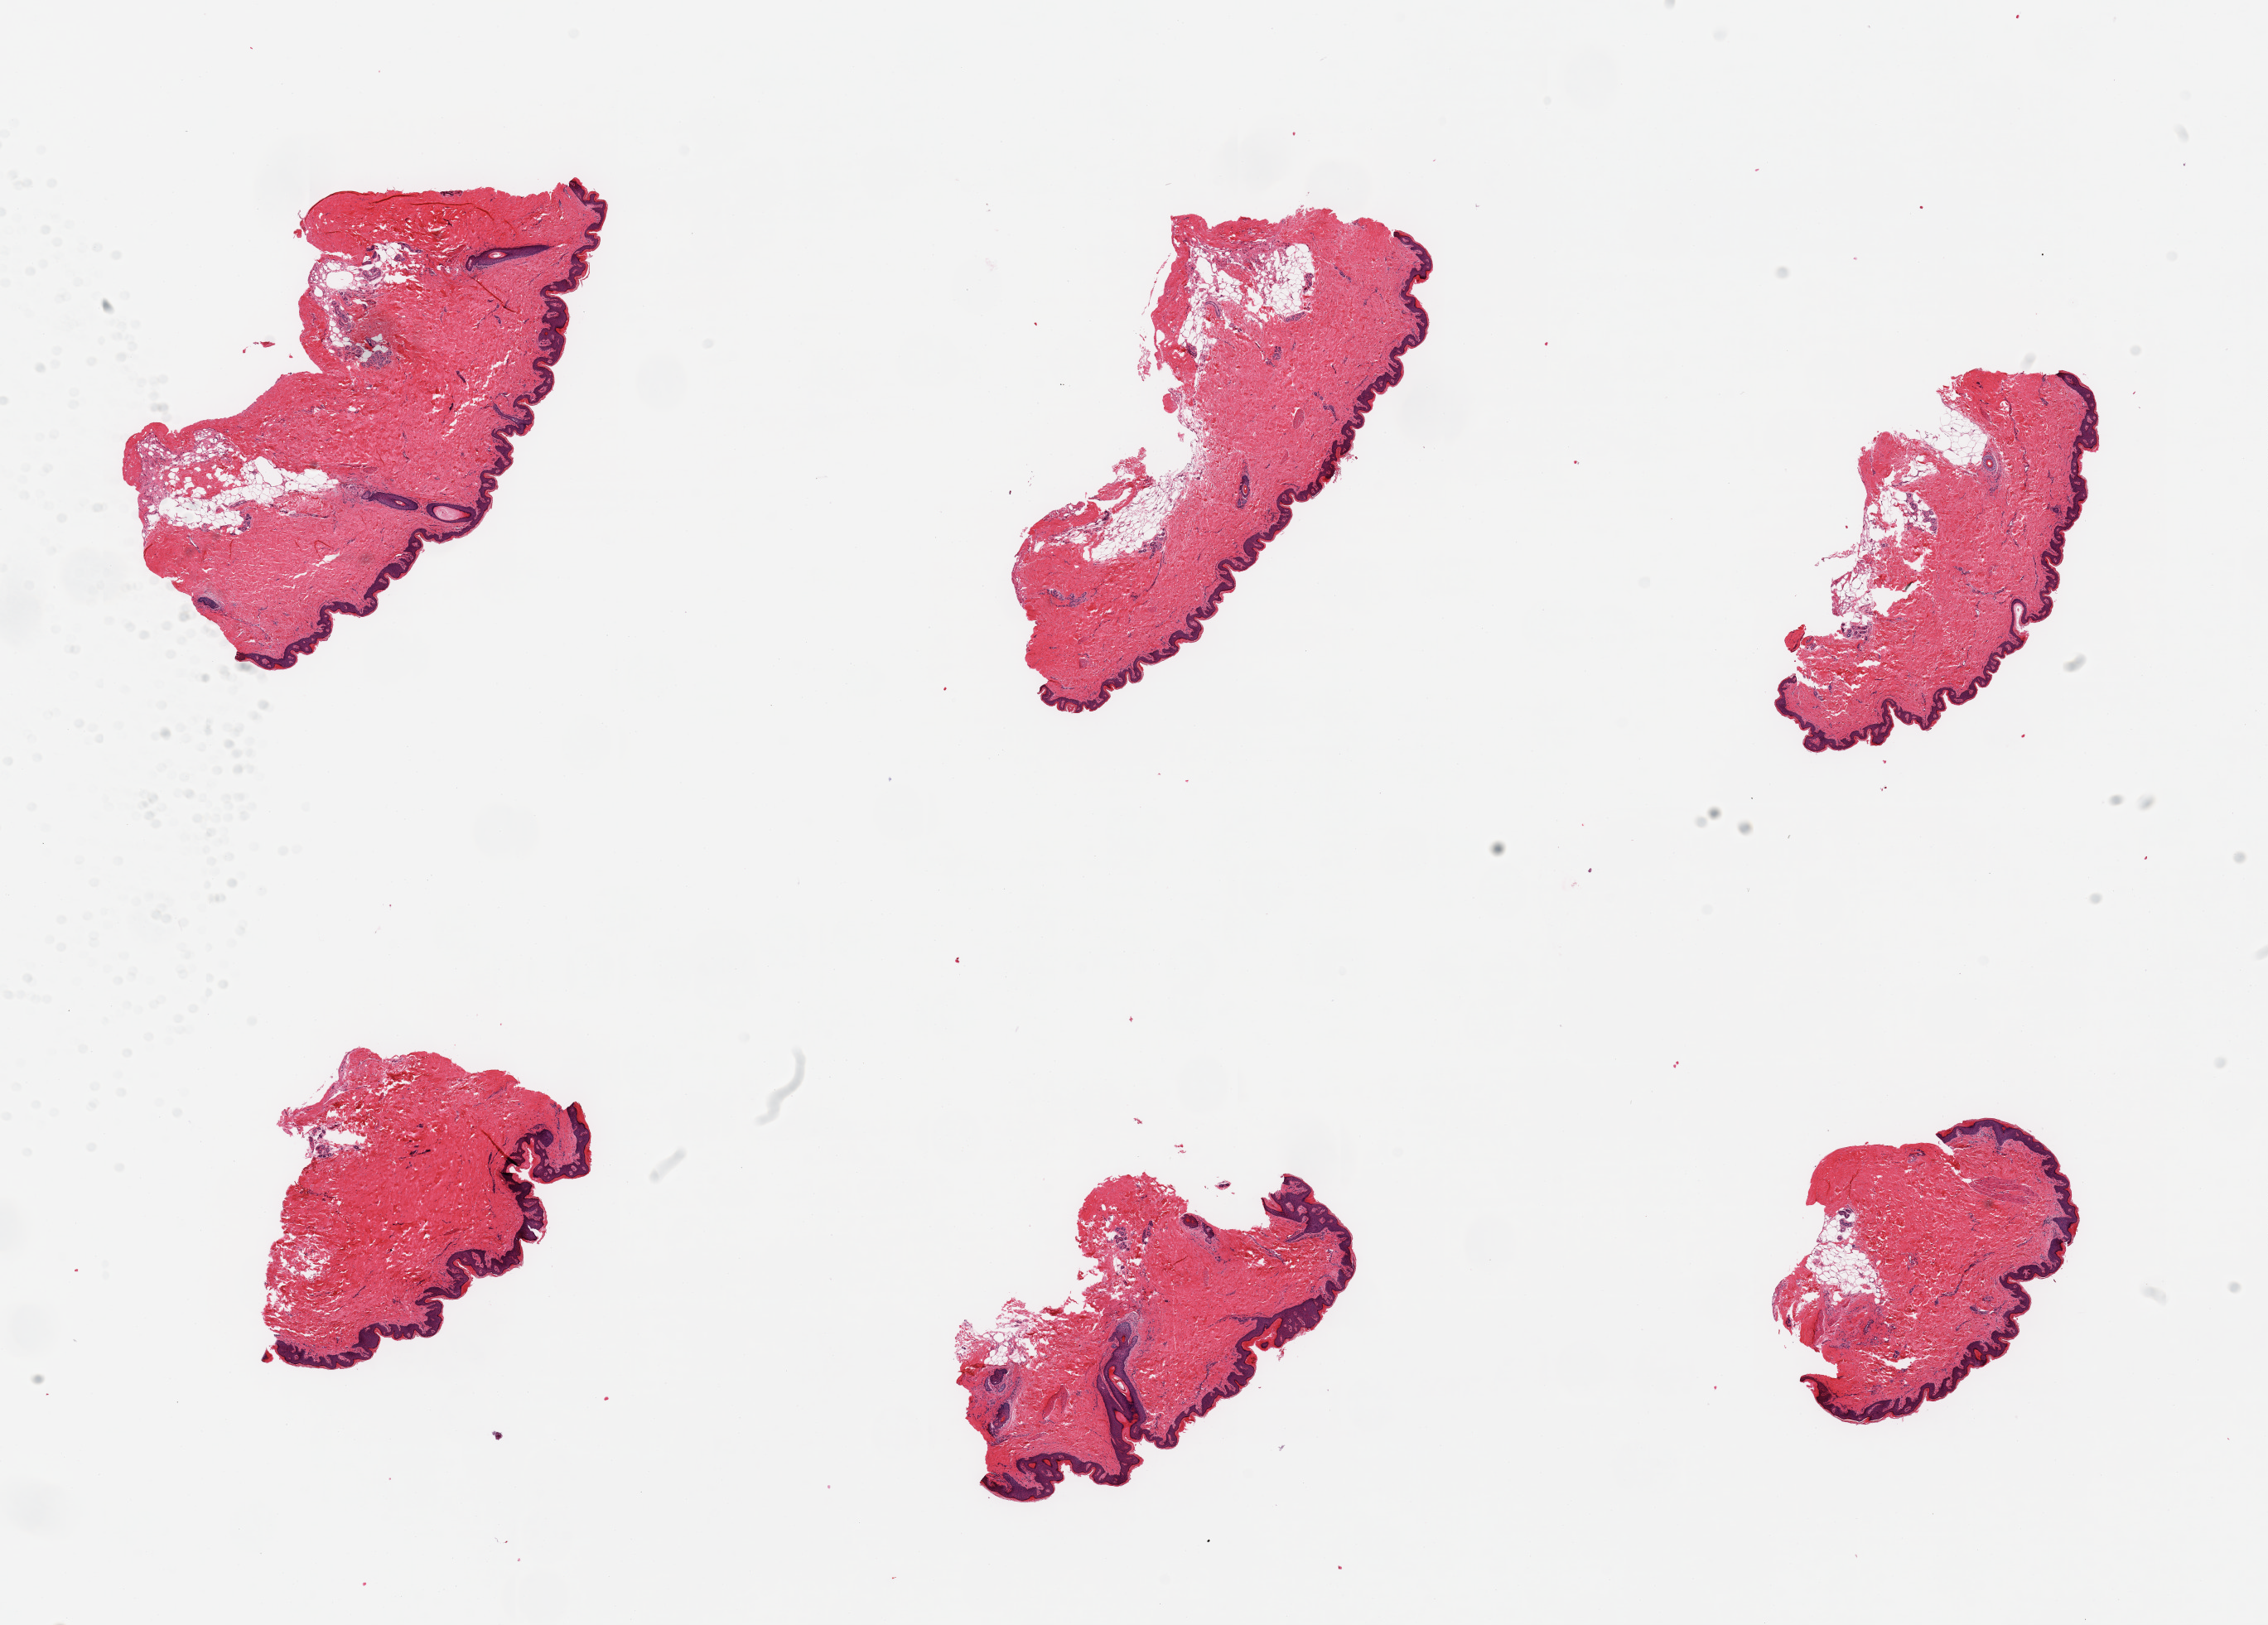
Digitized hematoxylin and eosin (H&E)-stained section, brightfield — shown as a low-resolution overview of the whole scanned area (about 21.7 x 15.5 mm); PAXgene-fixed, paraffin-embedded tissue; target tissue: skin of suprapubic region; tissue donor sample.
• reviewer comment on this tissue sample: 6 pieces; 10% dermal fat